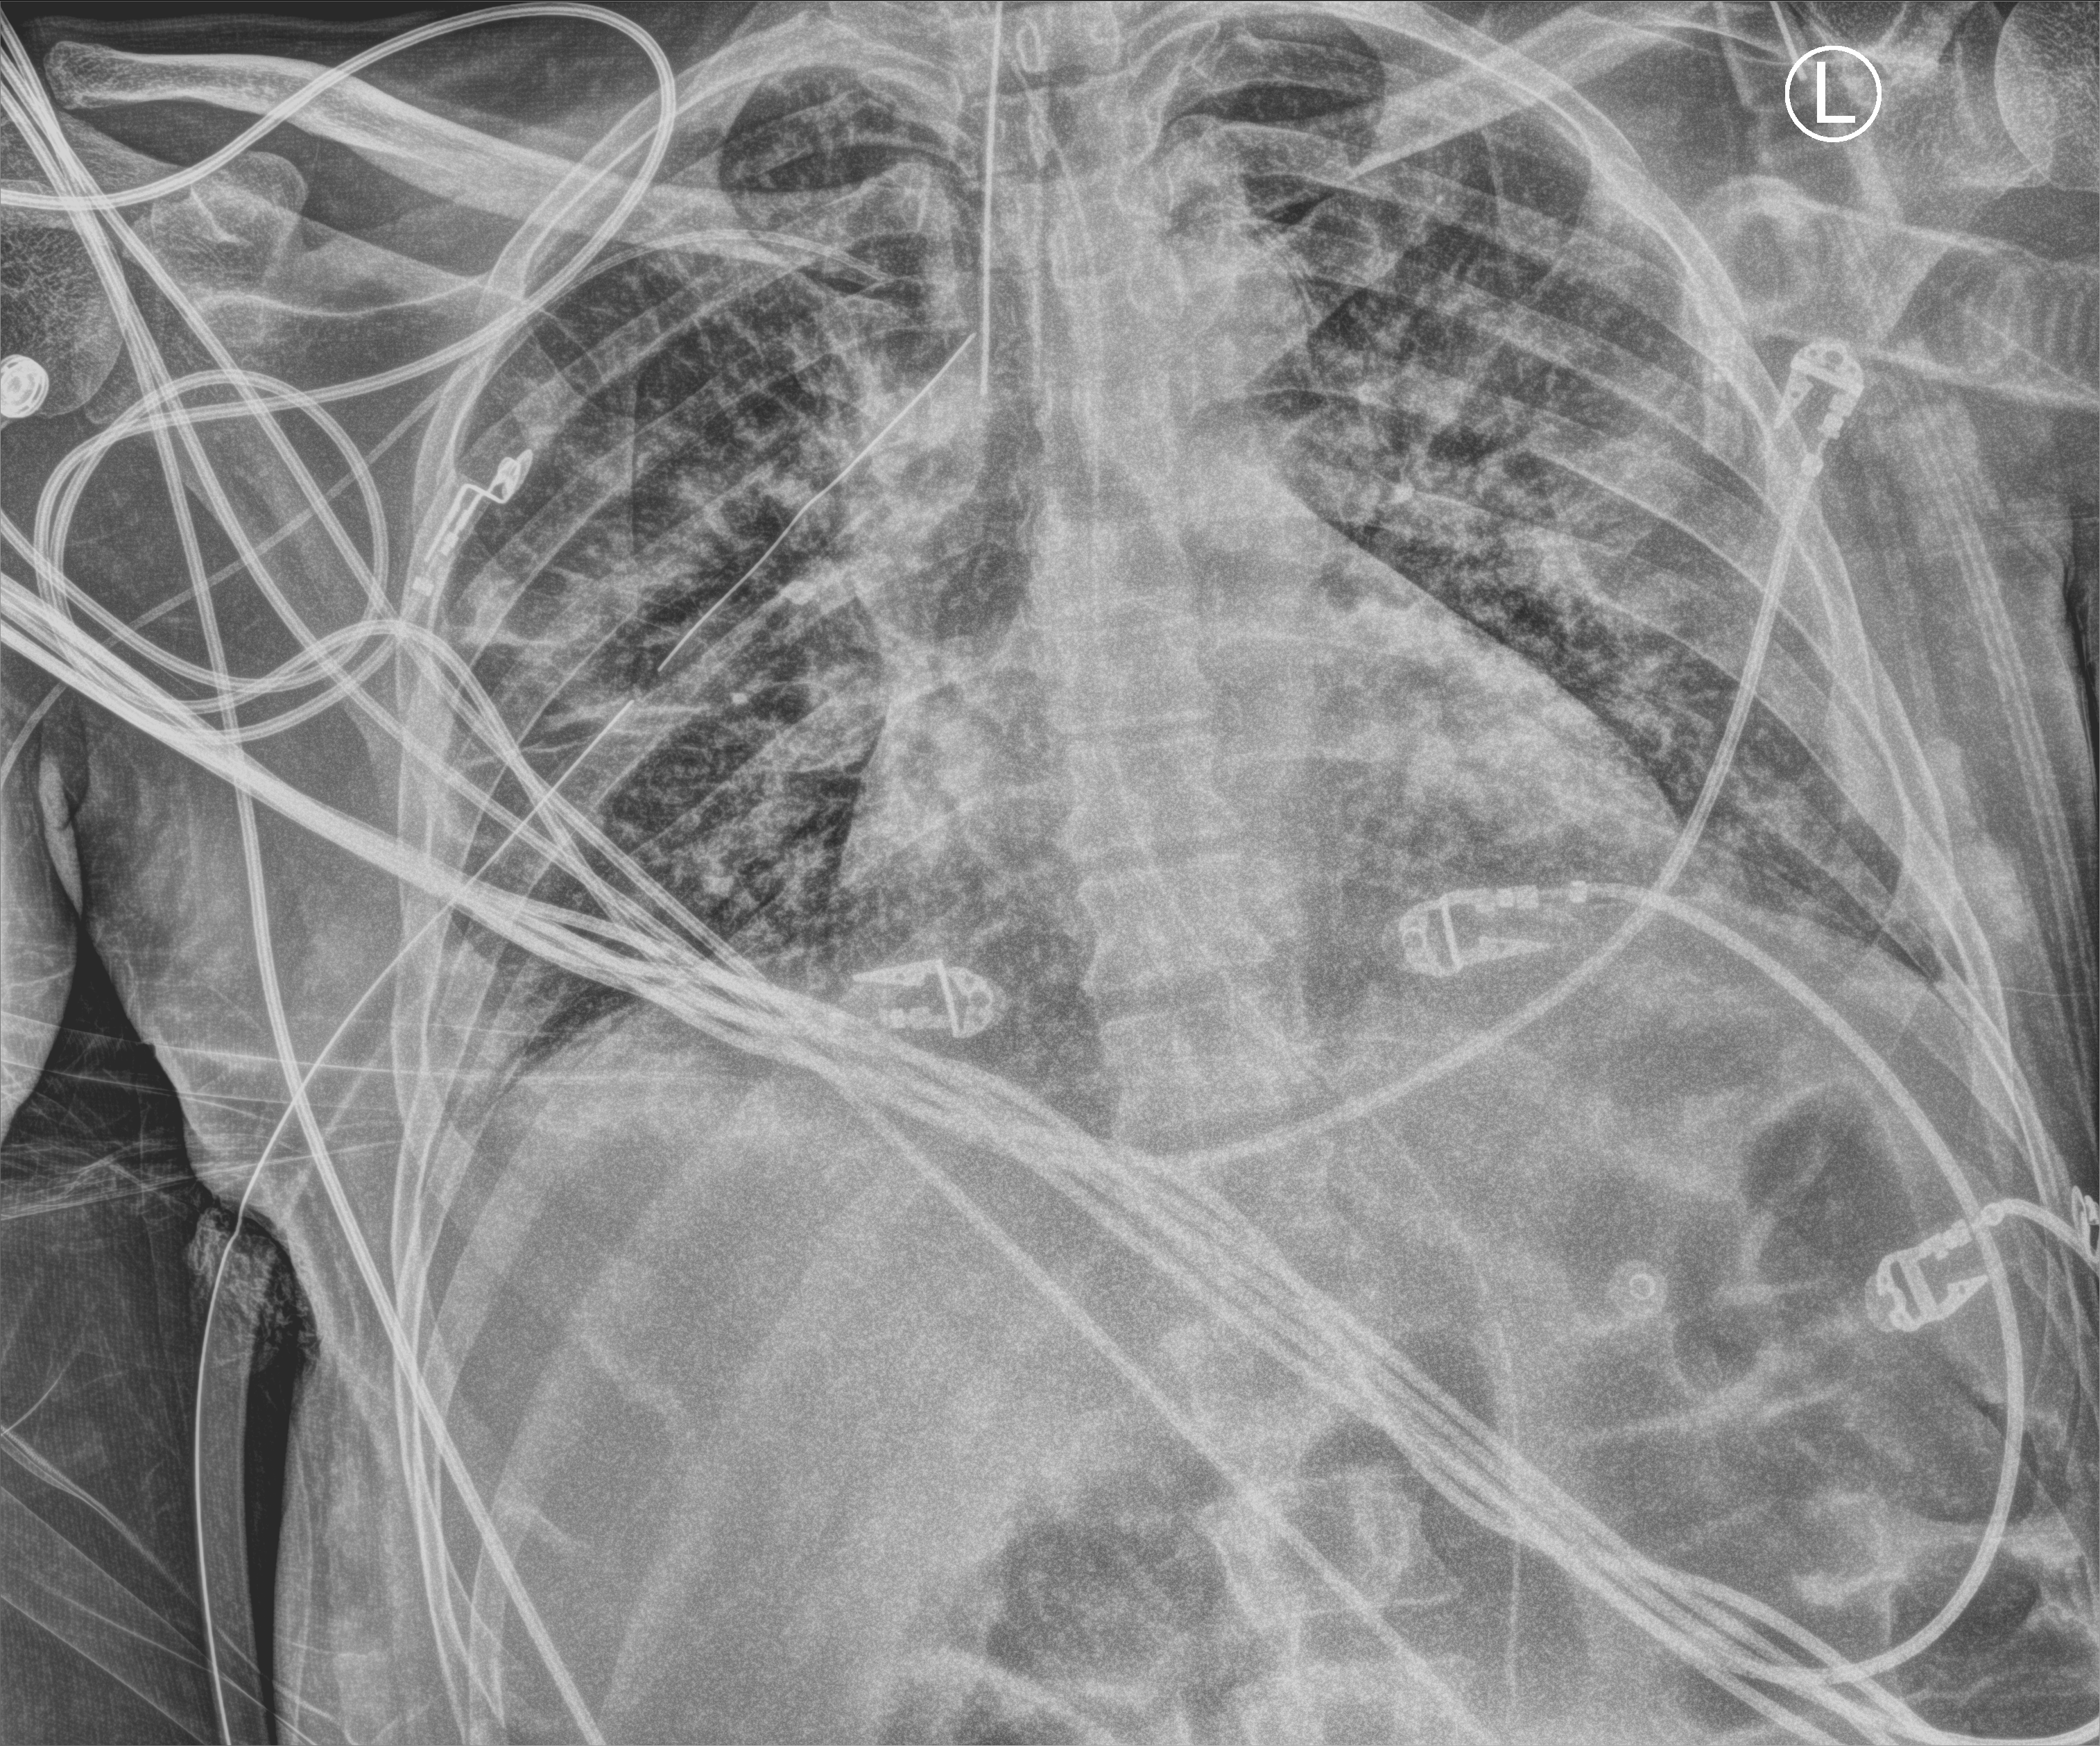
Chest X-ray (portable); anteroposterior (AP) projection. Patient hospitalised with COVID-19; male, aged 18–59 years.
Admission-level facts for this patient (not findings on this image; timing relative to this image not recorded): length of hospital stay: 41 days; admitted to intensive care during this hospital stay: yes; mechanically ventilated during this hospital stay: yes.